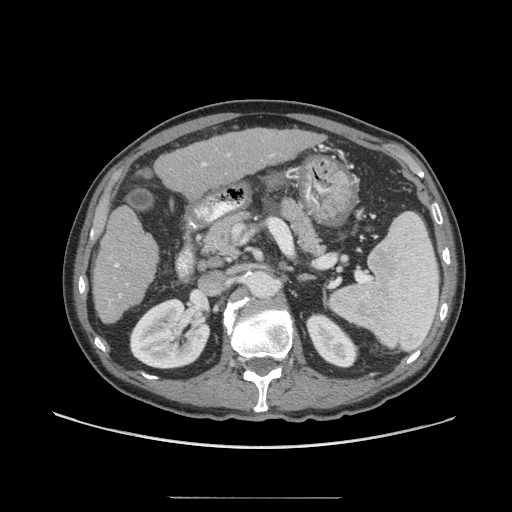
Contrast-enhanced abdominal CT (liver protocol), one axial slice; slice 28 of 71 in the series (ordered by position); reconstruction kernel STANDARD; 140 kVp; soft-tissue window (W 400 / L 40 HU); 512 × 512 image matrix. Case-level facts recorded for this patient, not image findings: diagnosis: hepatocellular carcinoma (patient treated with transarterial chemoembolisation; whether this scan precedes or follows treatment is not stated here); TNM stage (as recorded): Stage-I; Child-Pugh class: A; tumour differentiation: well differentiated; tumour nodularity: uninodular.
Structures marked on this image (semi-automatic segmentation, software-assisted and operator-edited):
- liver parenchyma outside the tumour (the mass and vessels are separate outlines, so this box may not span the whole liver): bounding box <92,128,316,324> (left, top, right, bottom; pixels)
- liver vessels: <109,153,273,302>